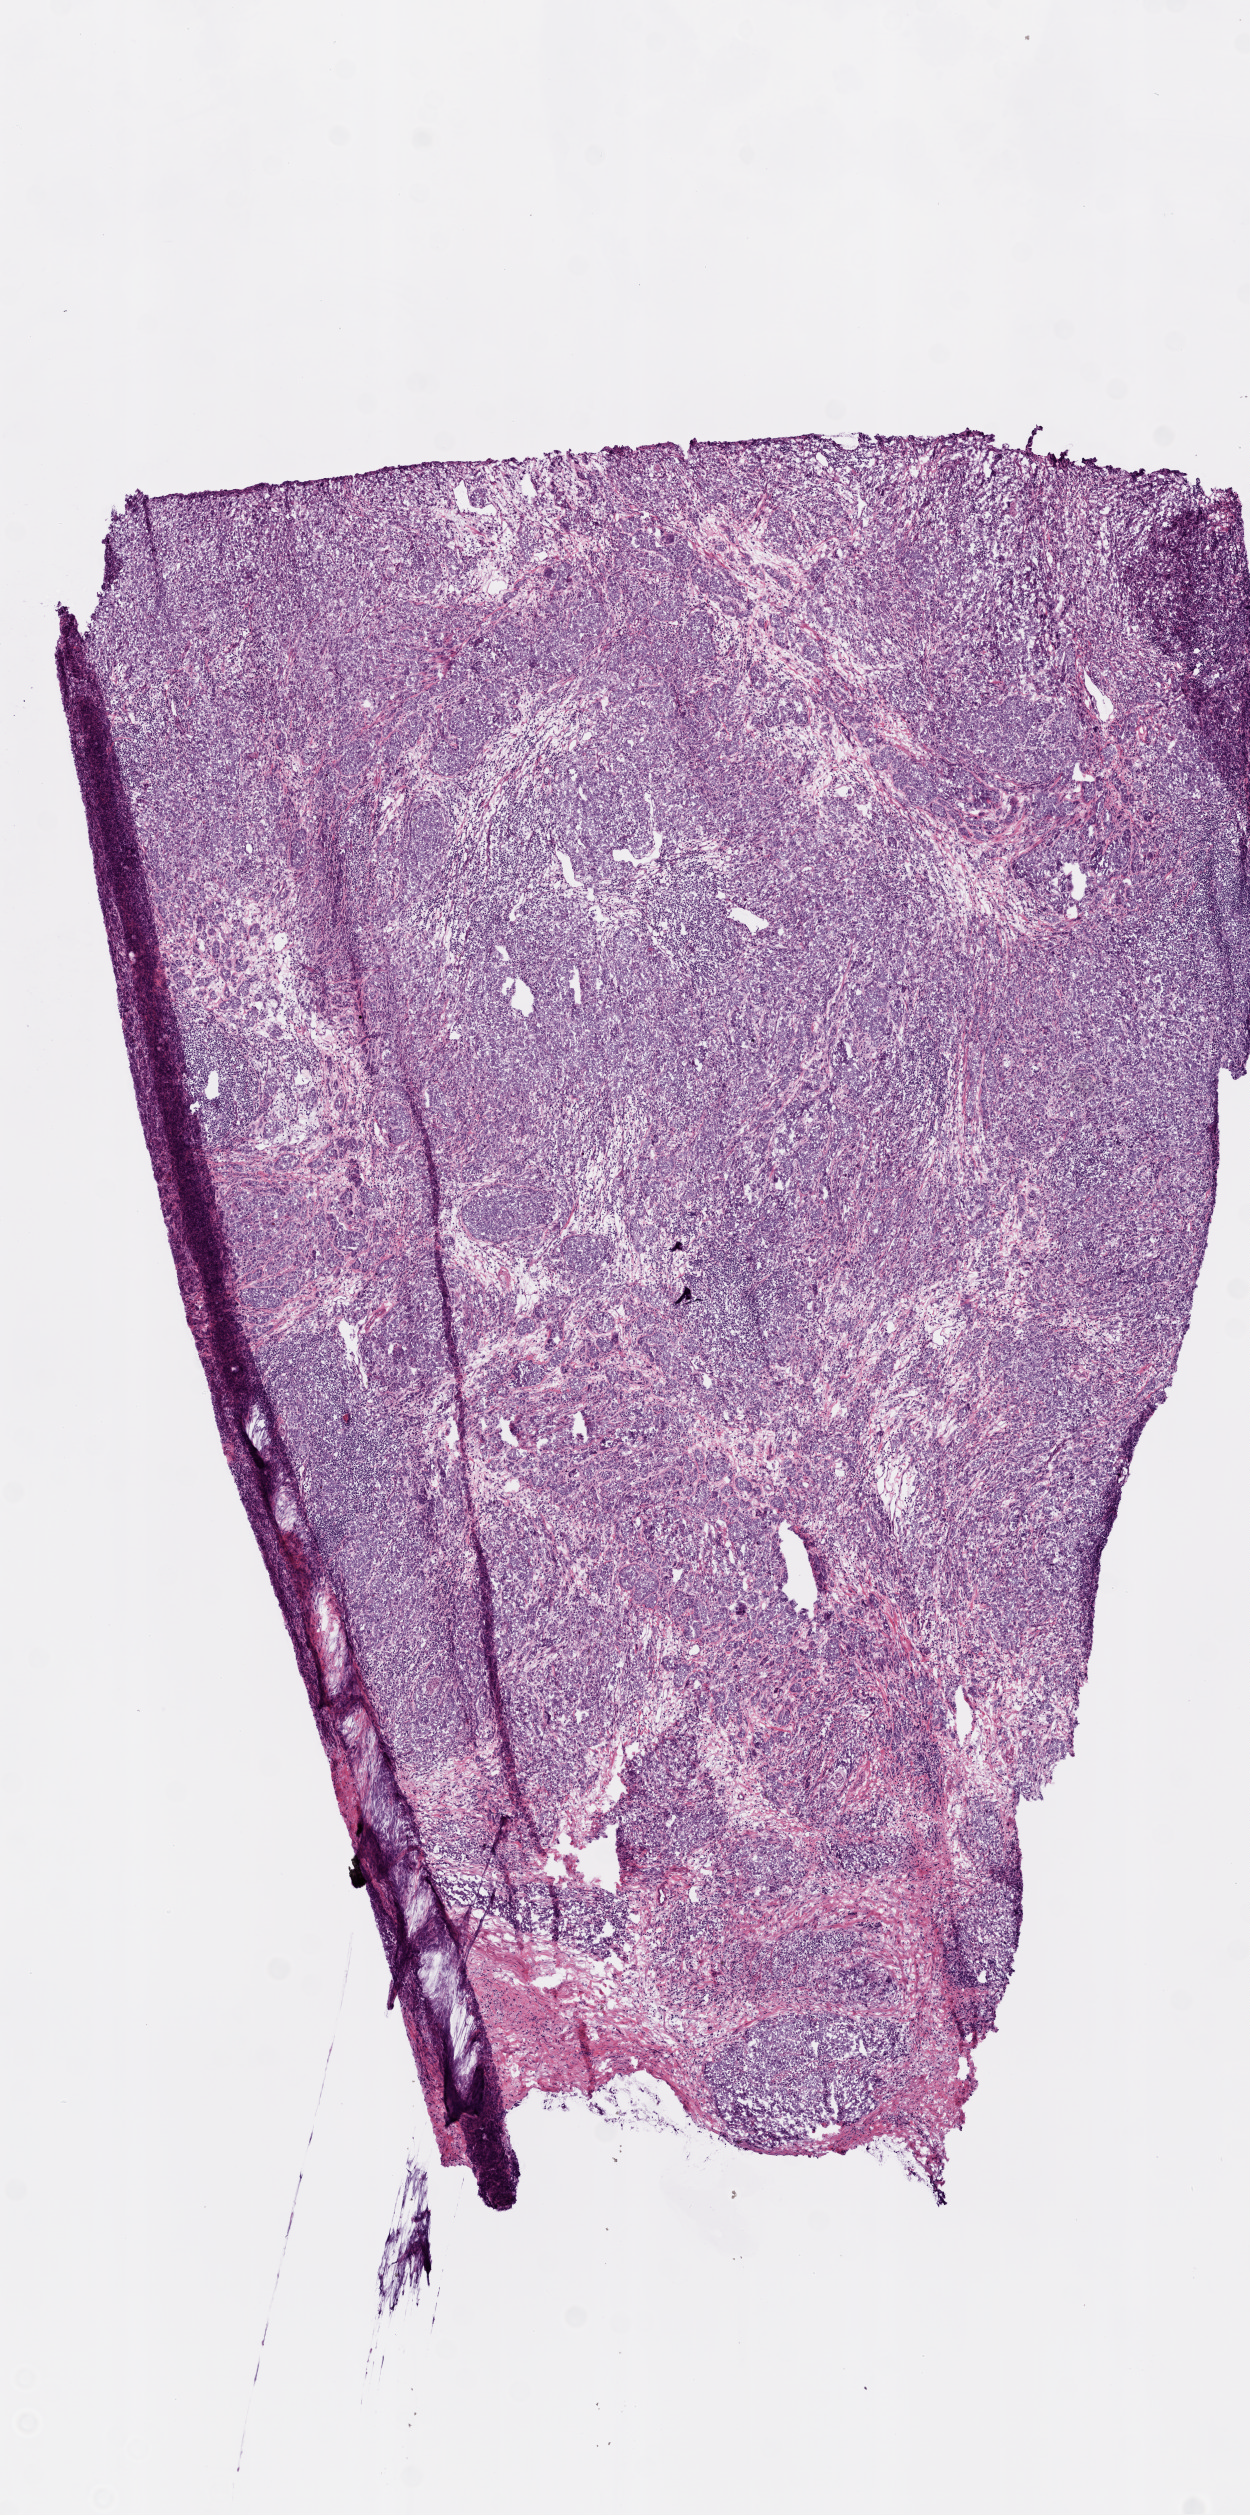
Digitized H&E-stained tissue section (whole slide) — a low-resolution overview of the entire scanned area, about 5.0 x 10.1 mm (slide scanned at 20x); frozen section from the bottom of the tissue portion; primary tumour sample from the prostate. Male, age 68 years at initial diagnosis. Gleason score: 10 (5+5). Pathologist review of this section (percent, as recorded): tumour cells 85%, tumour nuclei 95%, normal cells 0%, stromal cells 15%, necrosis 0%. Inflammatory infiltration, as recorded: lymphocyte infiltration 3%, monocyte infiltration 0%, neutrophil infiltration 0%.
Lymph nodes positive (case pathology): 1 of 3 examined. Pathologic diagnosis: Acinar cell carcinoma (prostate gland).